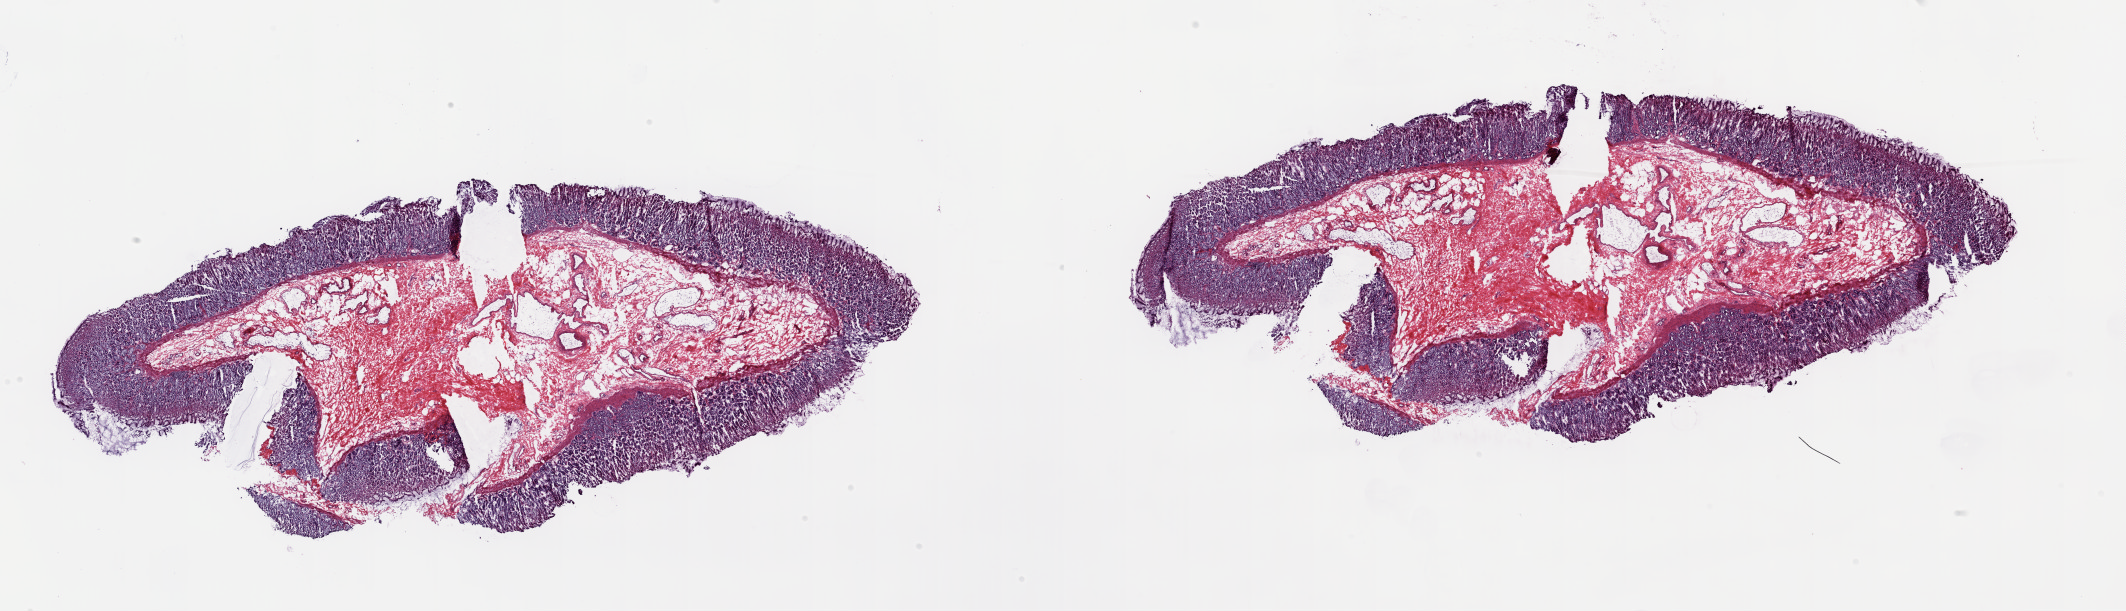
Hematoxylin and eosin (H&E) stained whole-slide image — shown as a low-resolution overview of the whole scanned area (about 33.7 x 9.7 mm). Frozen section from the top of the tissue portion. Solid tissue normal (non-tumour tissue) sample from the esophagus. Patient: male, age at initial diagnosis 44 years.
This section: solid tissue normal sample (biorepository sample class). Patient diagnosis: Adenocarcinoma, NOS (lower third of esophagus).